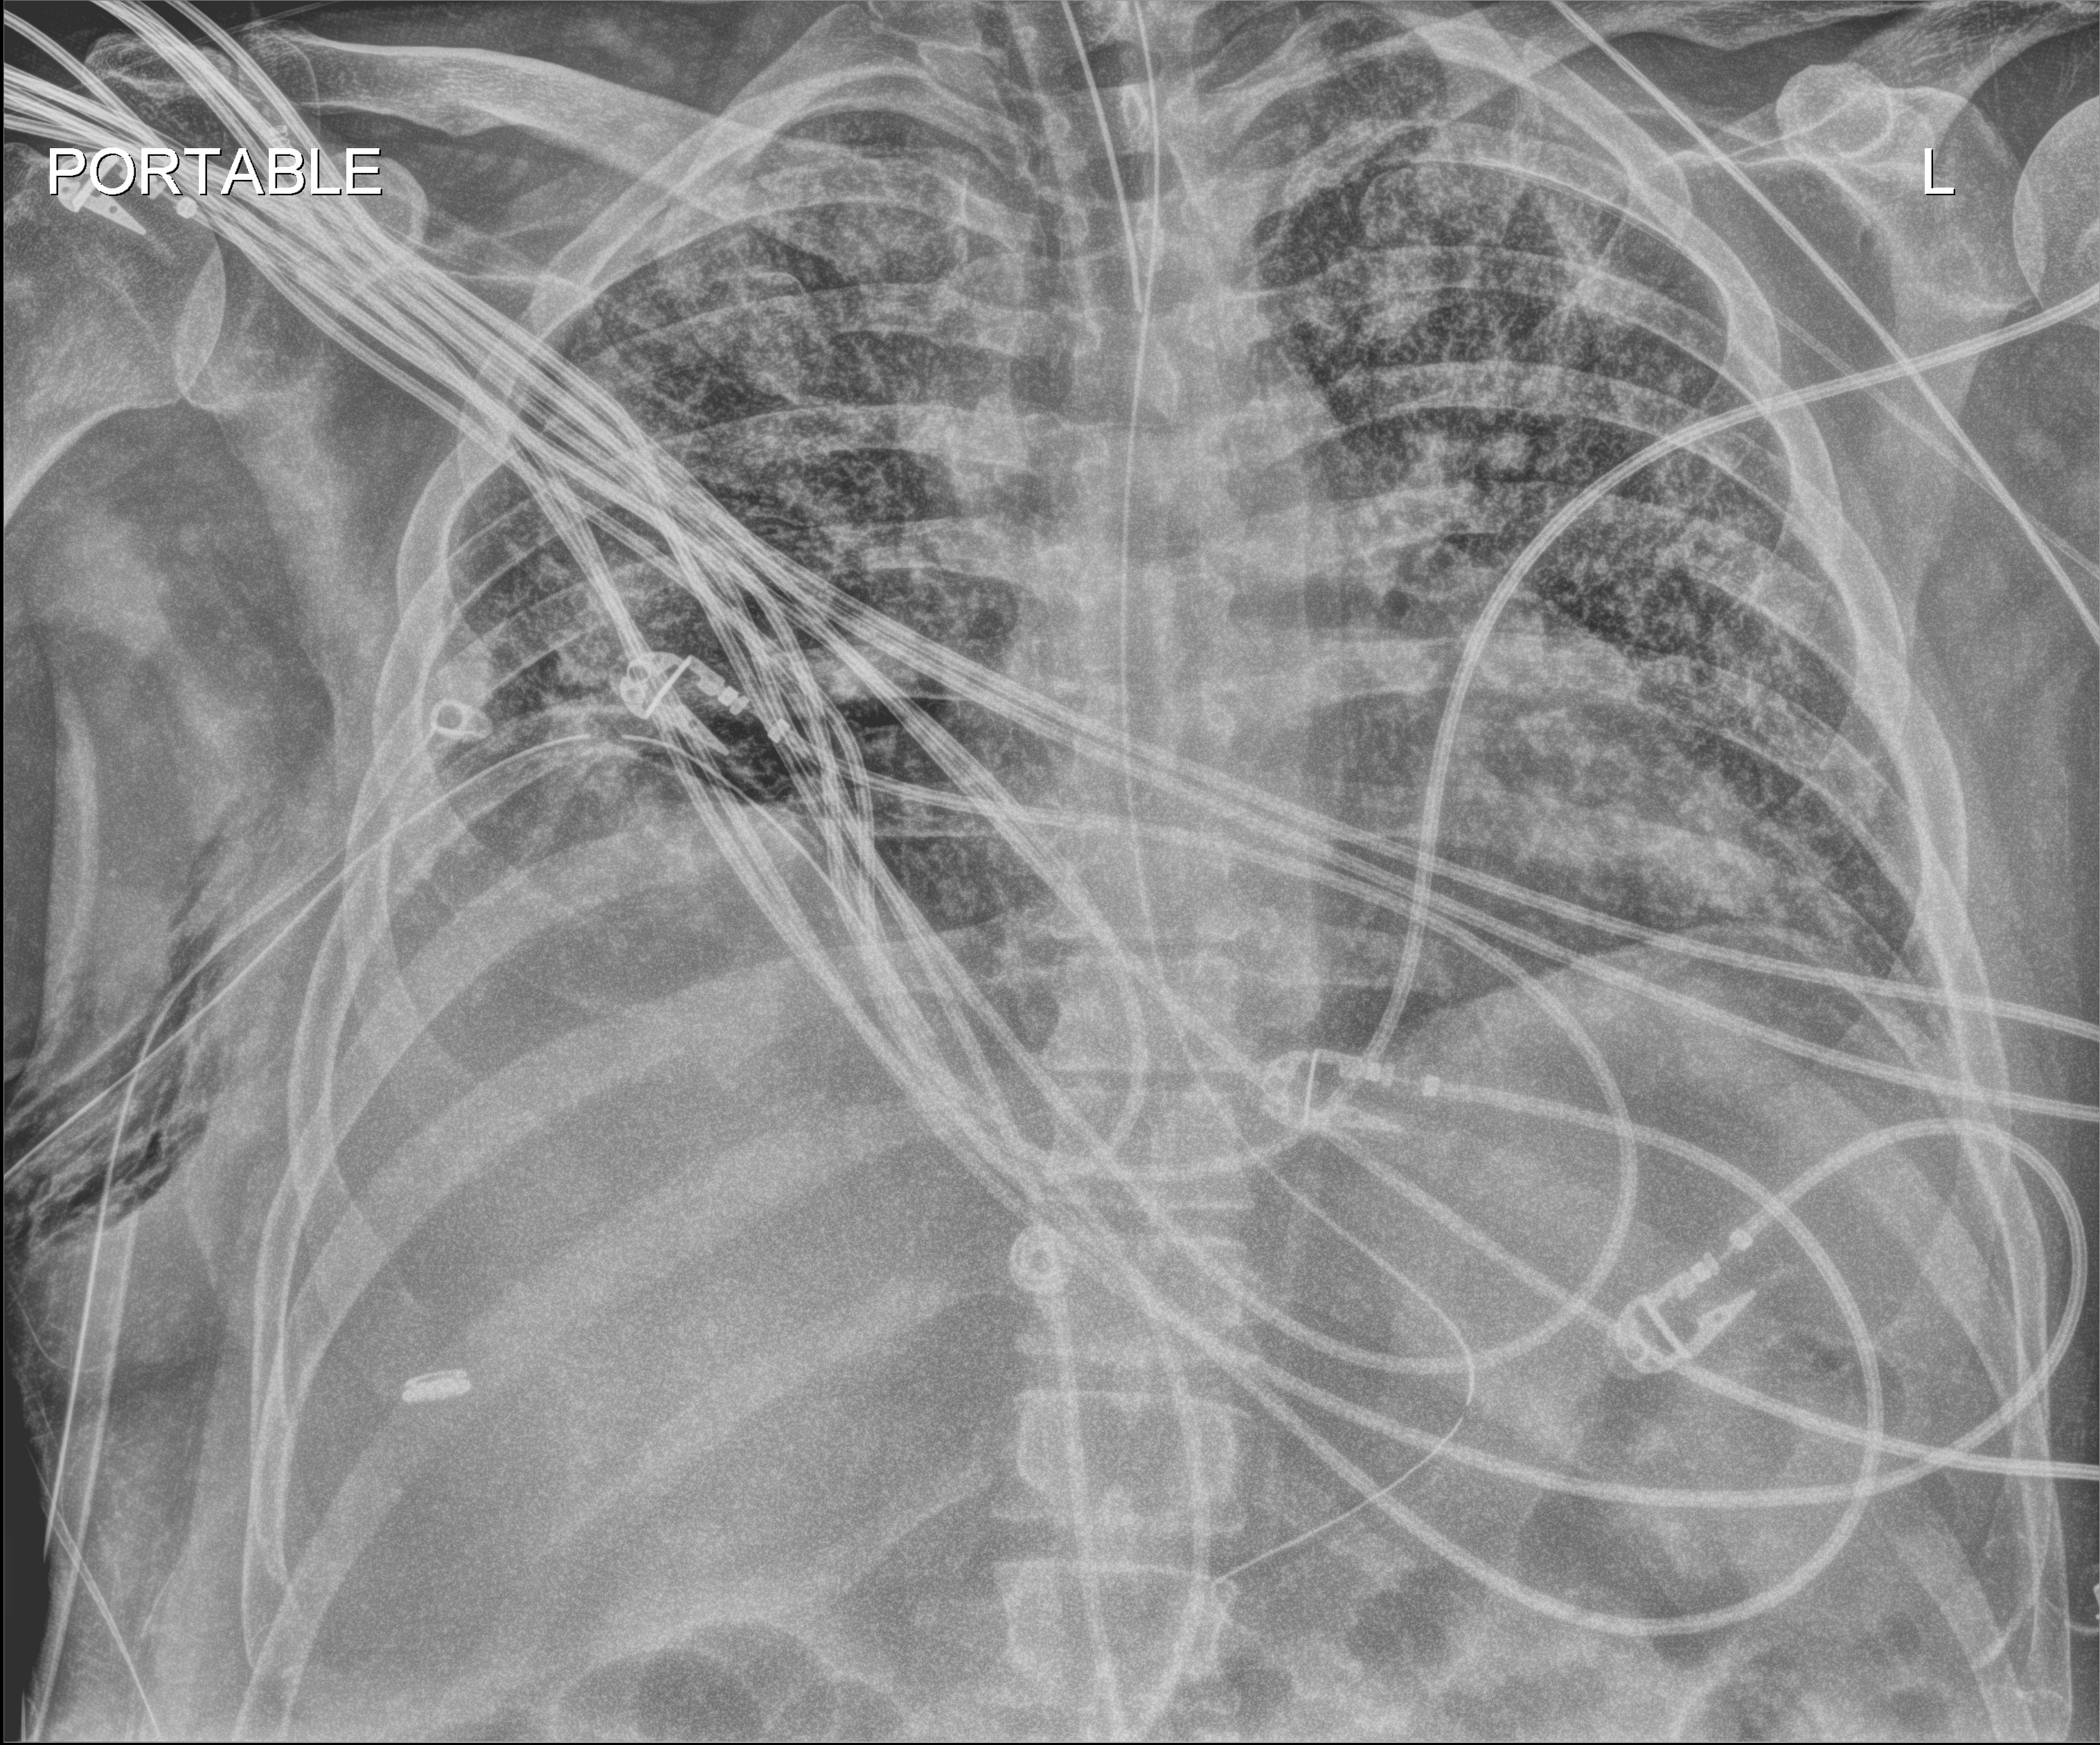
Chest X-ray (portable), anteroposterior (AP) projection. Male patient hospitalised with COVID-19, age 18–59 years.
Admission-level facts for this patient (not findings on this image; timing relative to this image not recorded): admitted to intensive care during this hospital stay: yes; mechanically ventilated during this hospital stay: yes.